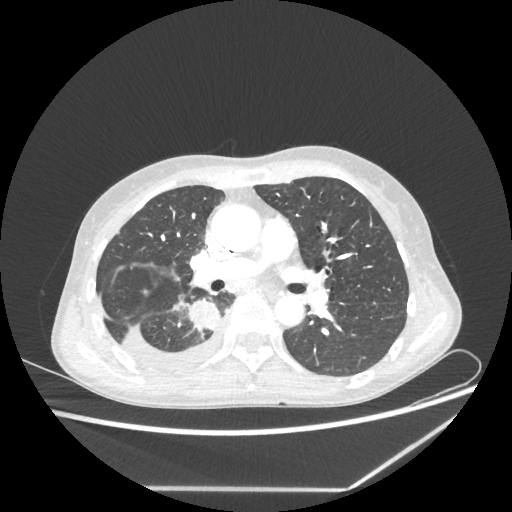
Chest CT, one axial slice. Position 133 of 237 along the scan axis. 80 kVp. Lung window (W 1500 / L -600 HU). 512 × 512 image matrix. Patient: female, 59 years. From the clinical record (not read from this slice): clinical TNM (as recorded): T1c N1 M1.
Annotated regions visible in this slice (rectangle marked by the reading radiologist):
- lung tumour (recorded histology: adenocarcinoma): bounding box (x1, y1, x2, y2) in pixels: (184, 298, 221, 335)